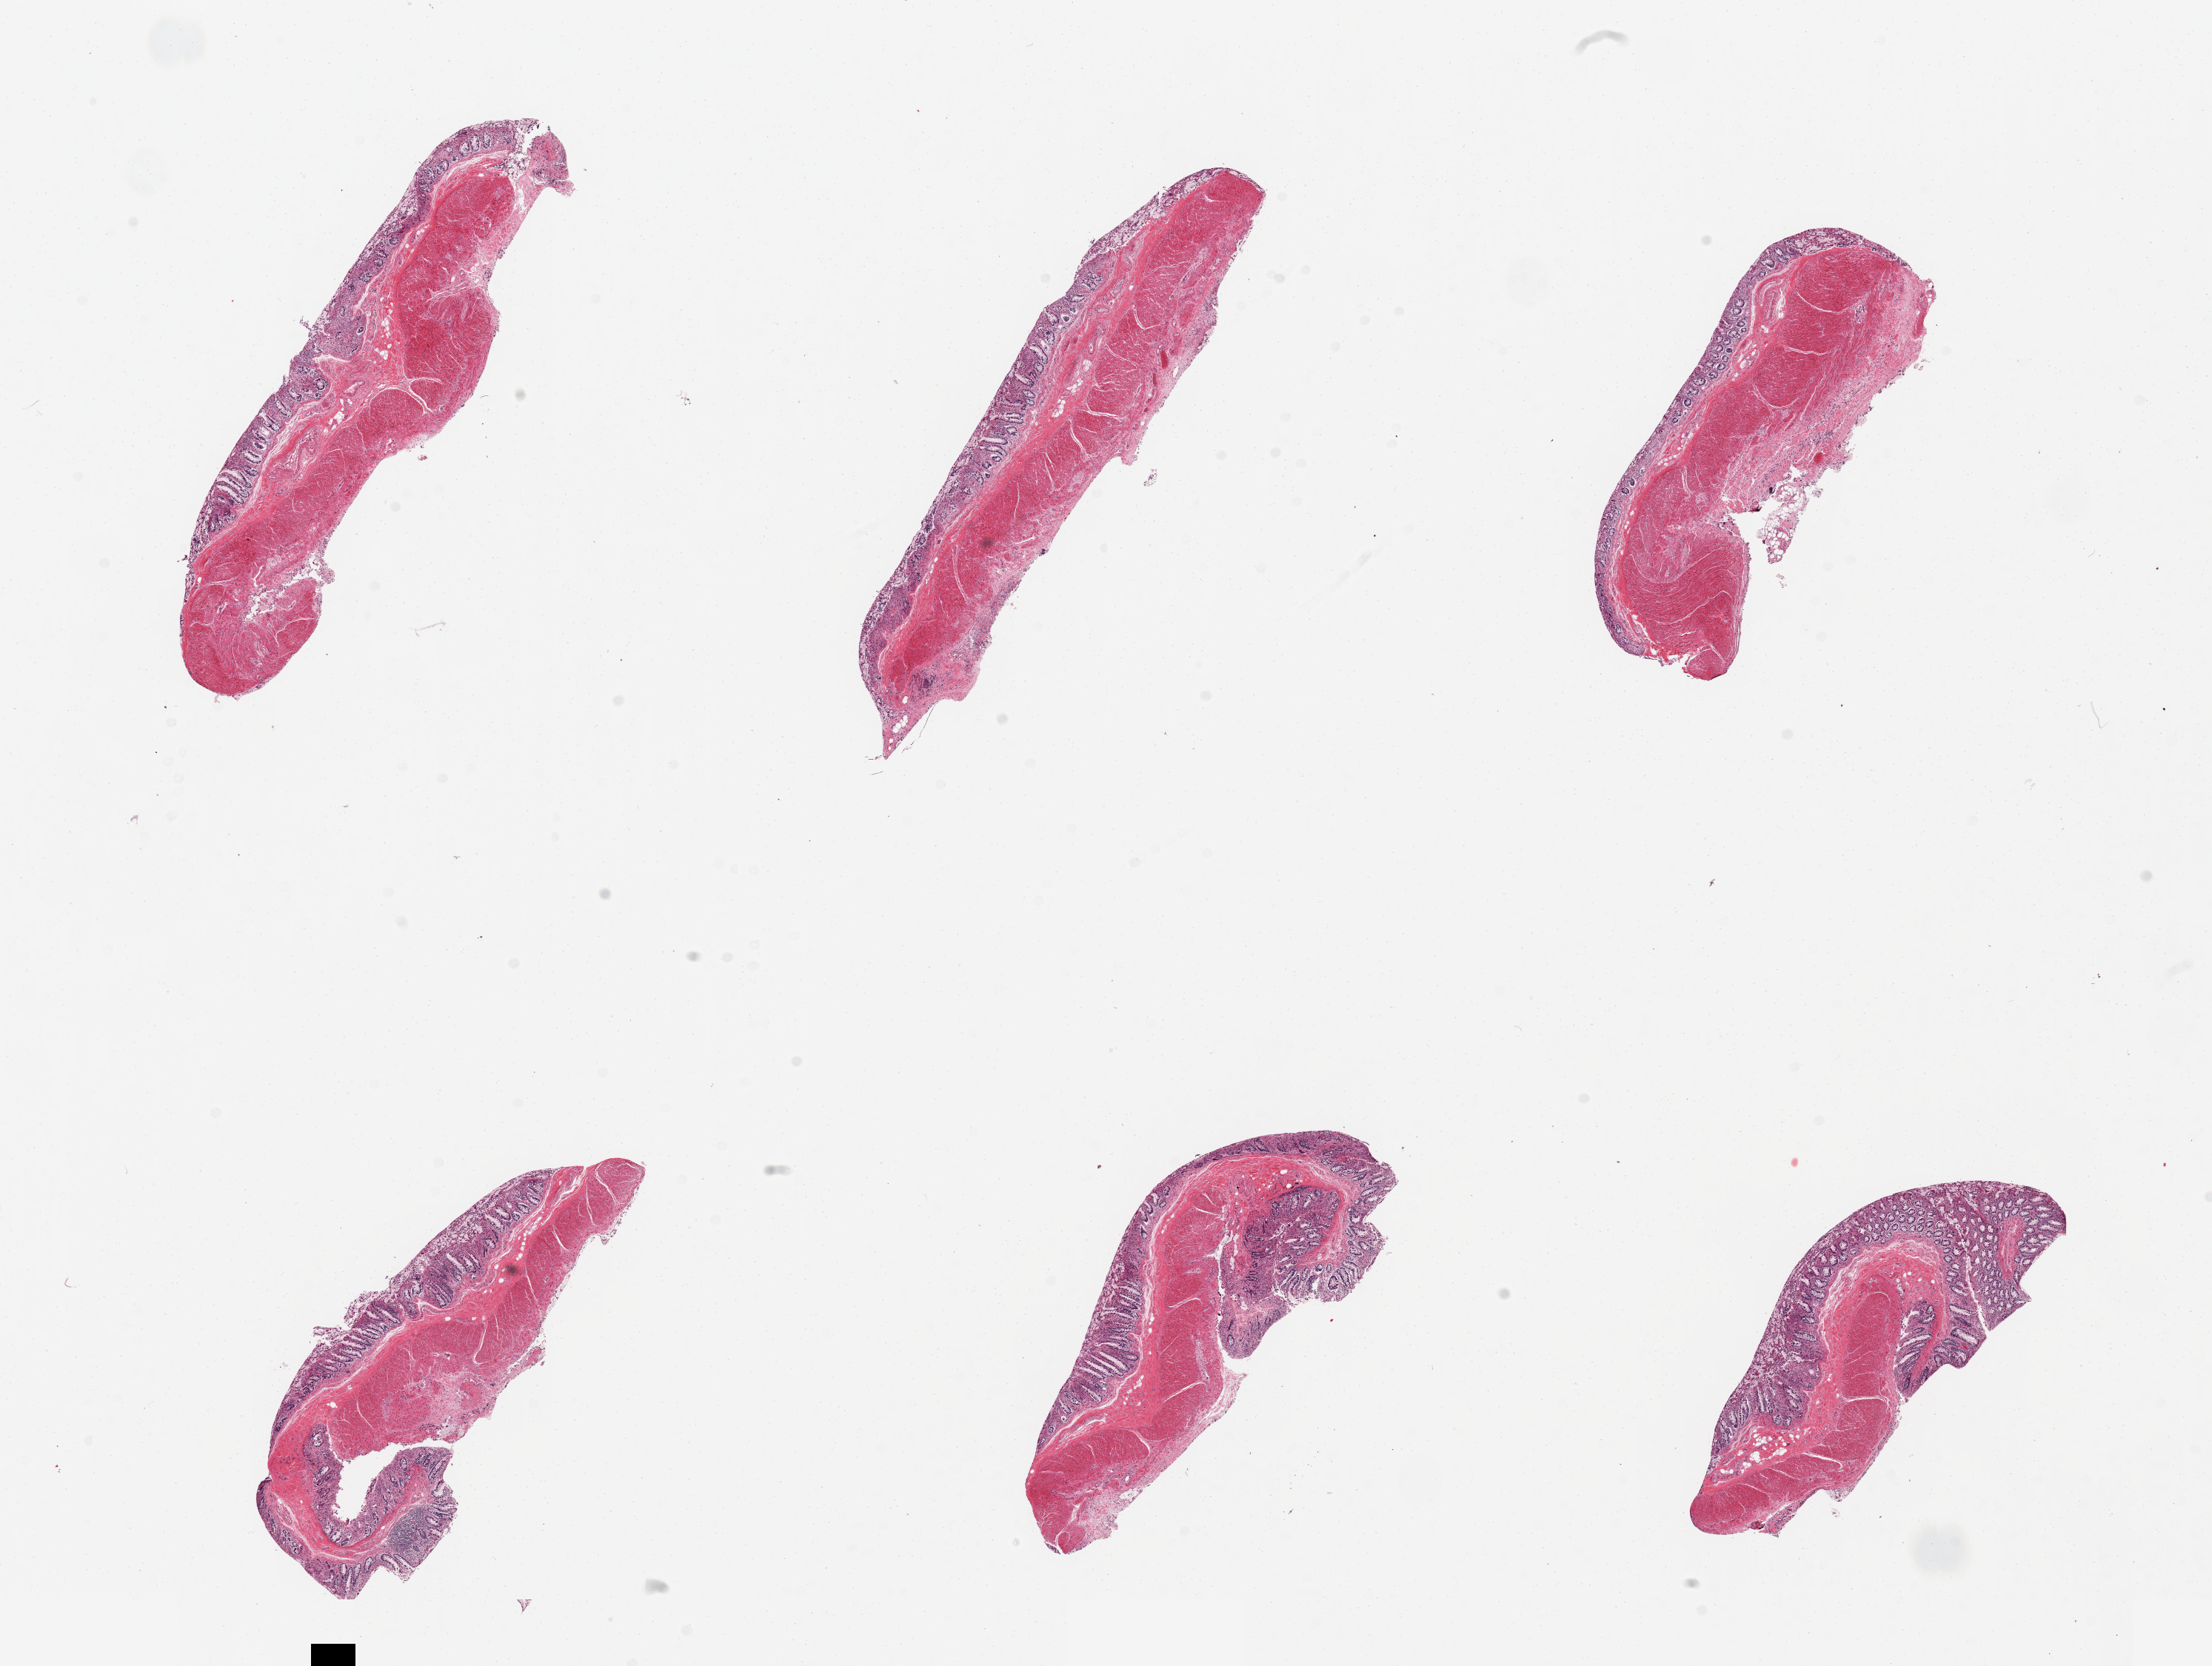
Whole-slide image, haematoxylin and eosin stain — whole scanned area (about 23.6 x 17.8 mm, slide scanned at 20x) shown as a low-resolution overview. PAXgene-fixed paraffin-embedded (PFPE) section. Target tissue: transverse colon. Tissue donor sample.
- reviewer comment on this tissue sample: 6 pieces